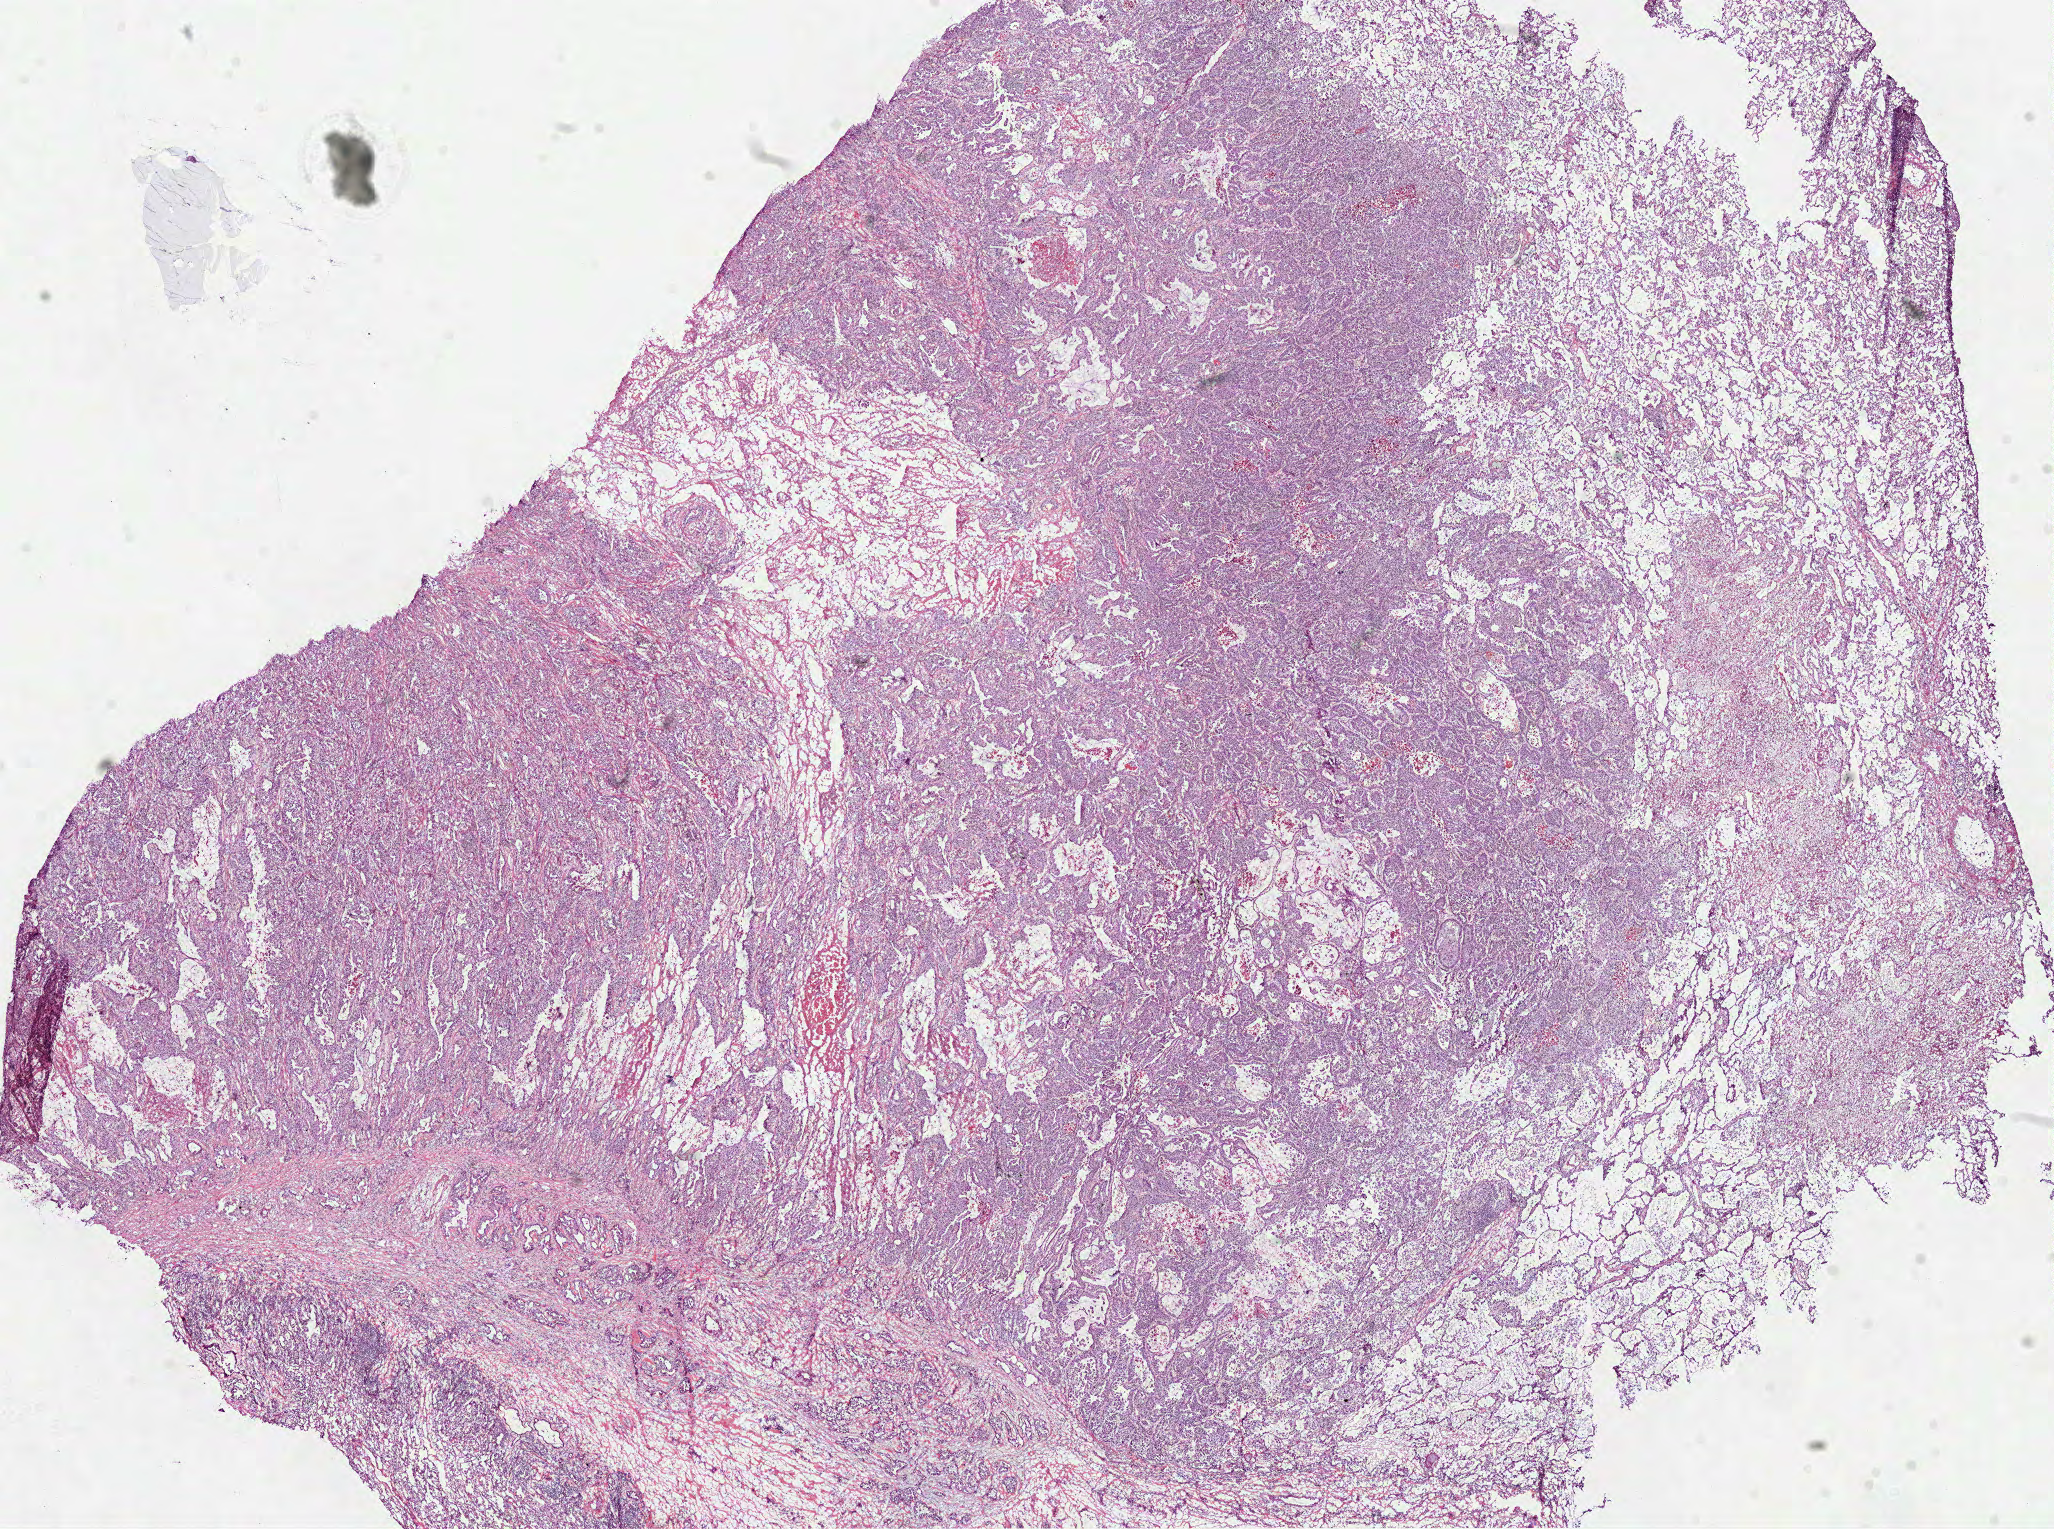
Digitized H&E tissue section (whole slide), low-resolution overview of the scanned area, about 16.6 x 12.3 mm (slide scanned at 40x), frozen section from the top of the tissue portion, sample: primary tumour, lung. Male, age 52 years at initial diagnosis. Pathologist review of this section (percent, as recorded): tumour cells 65%, tumour nuclei 75%, normal cells 15%, stromal cells 15%, necrosis 5%.
Laterality: right. TNM: T2a N1 M0. AJCC pathologic stage: IIA (7th edition). Histologic diagnosis: Adenocarcinoma, NOS (upper lobe, lung).